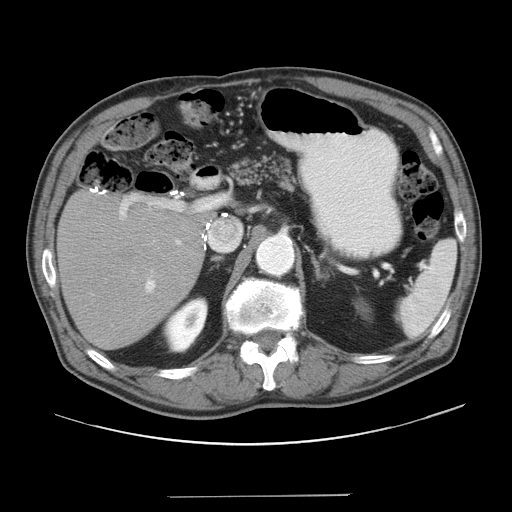
Contrast-enhanced abdominal CT, one axial slice. Slice 24 of 41 in the series (ordered by position). Reconstruction kernel STANDARD. 120 kVp. Intravenous contrast given. Soft-tissue window (W 400 / L 40 HU). 5 mm slice thickness. 512 × 512 image matrix, field of view 420 × 420 mm. Male patient, age 75 years. Case-level facts recorded for this patient, not image findings: diagnosis: colorectal cancer liver metastases, imaged before liver resection; multiple liver metastases: no; largest metastasis: 5.2 cm; disease in both lobes: no.
Outlined on this slice (expert manual segmentation):
- liver: box from (x=59, y=191) to (x=205, y=349) px
- planned liver remnant (the part of the liver to remain after resection): (x=58, y=191)–(x=205, y=349)
- portal vein (with intrahepatic branches): (x=111, y=200)–(x=196, y=327)